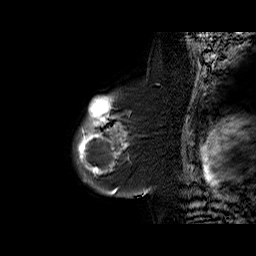
Breast MRI (dynamic contrast-enhanced), one sagittal slice. Slice 48 of 60 in the series (ordered by position). Dynamic contrast-enhanced series, time point 2 of 6 at this slice position (early post-contrast). 1.5 T. TE 6.3 ms, TR 32.4 ms. 4 mm slice thickness. 256 × 256 image matrix. Female patient. From the clinical record (not read from this slice): setting: breast cancer imaged before/during neoadjuvant chemotherapy; receptor status: triple-negative.
Outlined on this slice (semi-automatically segmented with operator editing):
- analysis volume of interest (the breast-tissue region the enhancement analysis was run in; not a lesion): box from (x=72, y=93) to (x=145, y=187) px
- tumour enhancement mask (voxels above the 100 % enhancement threshold inside the analysis volume of interest): (x=77, y=96)–(x=128, y=174)